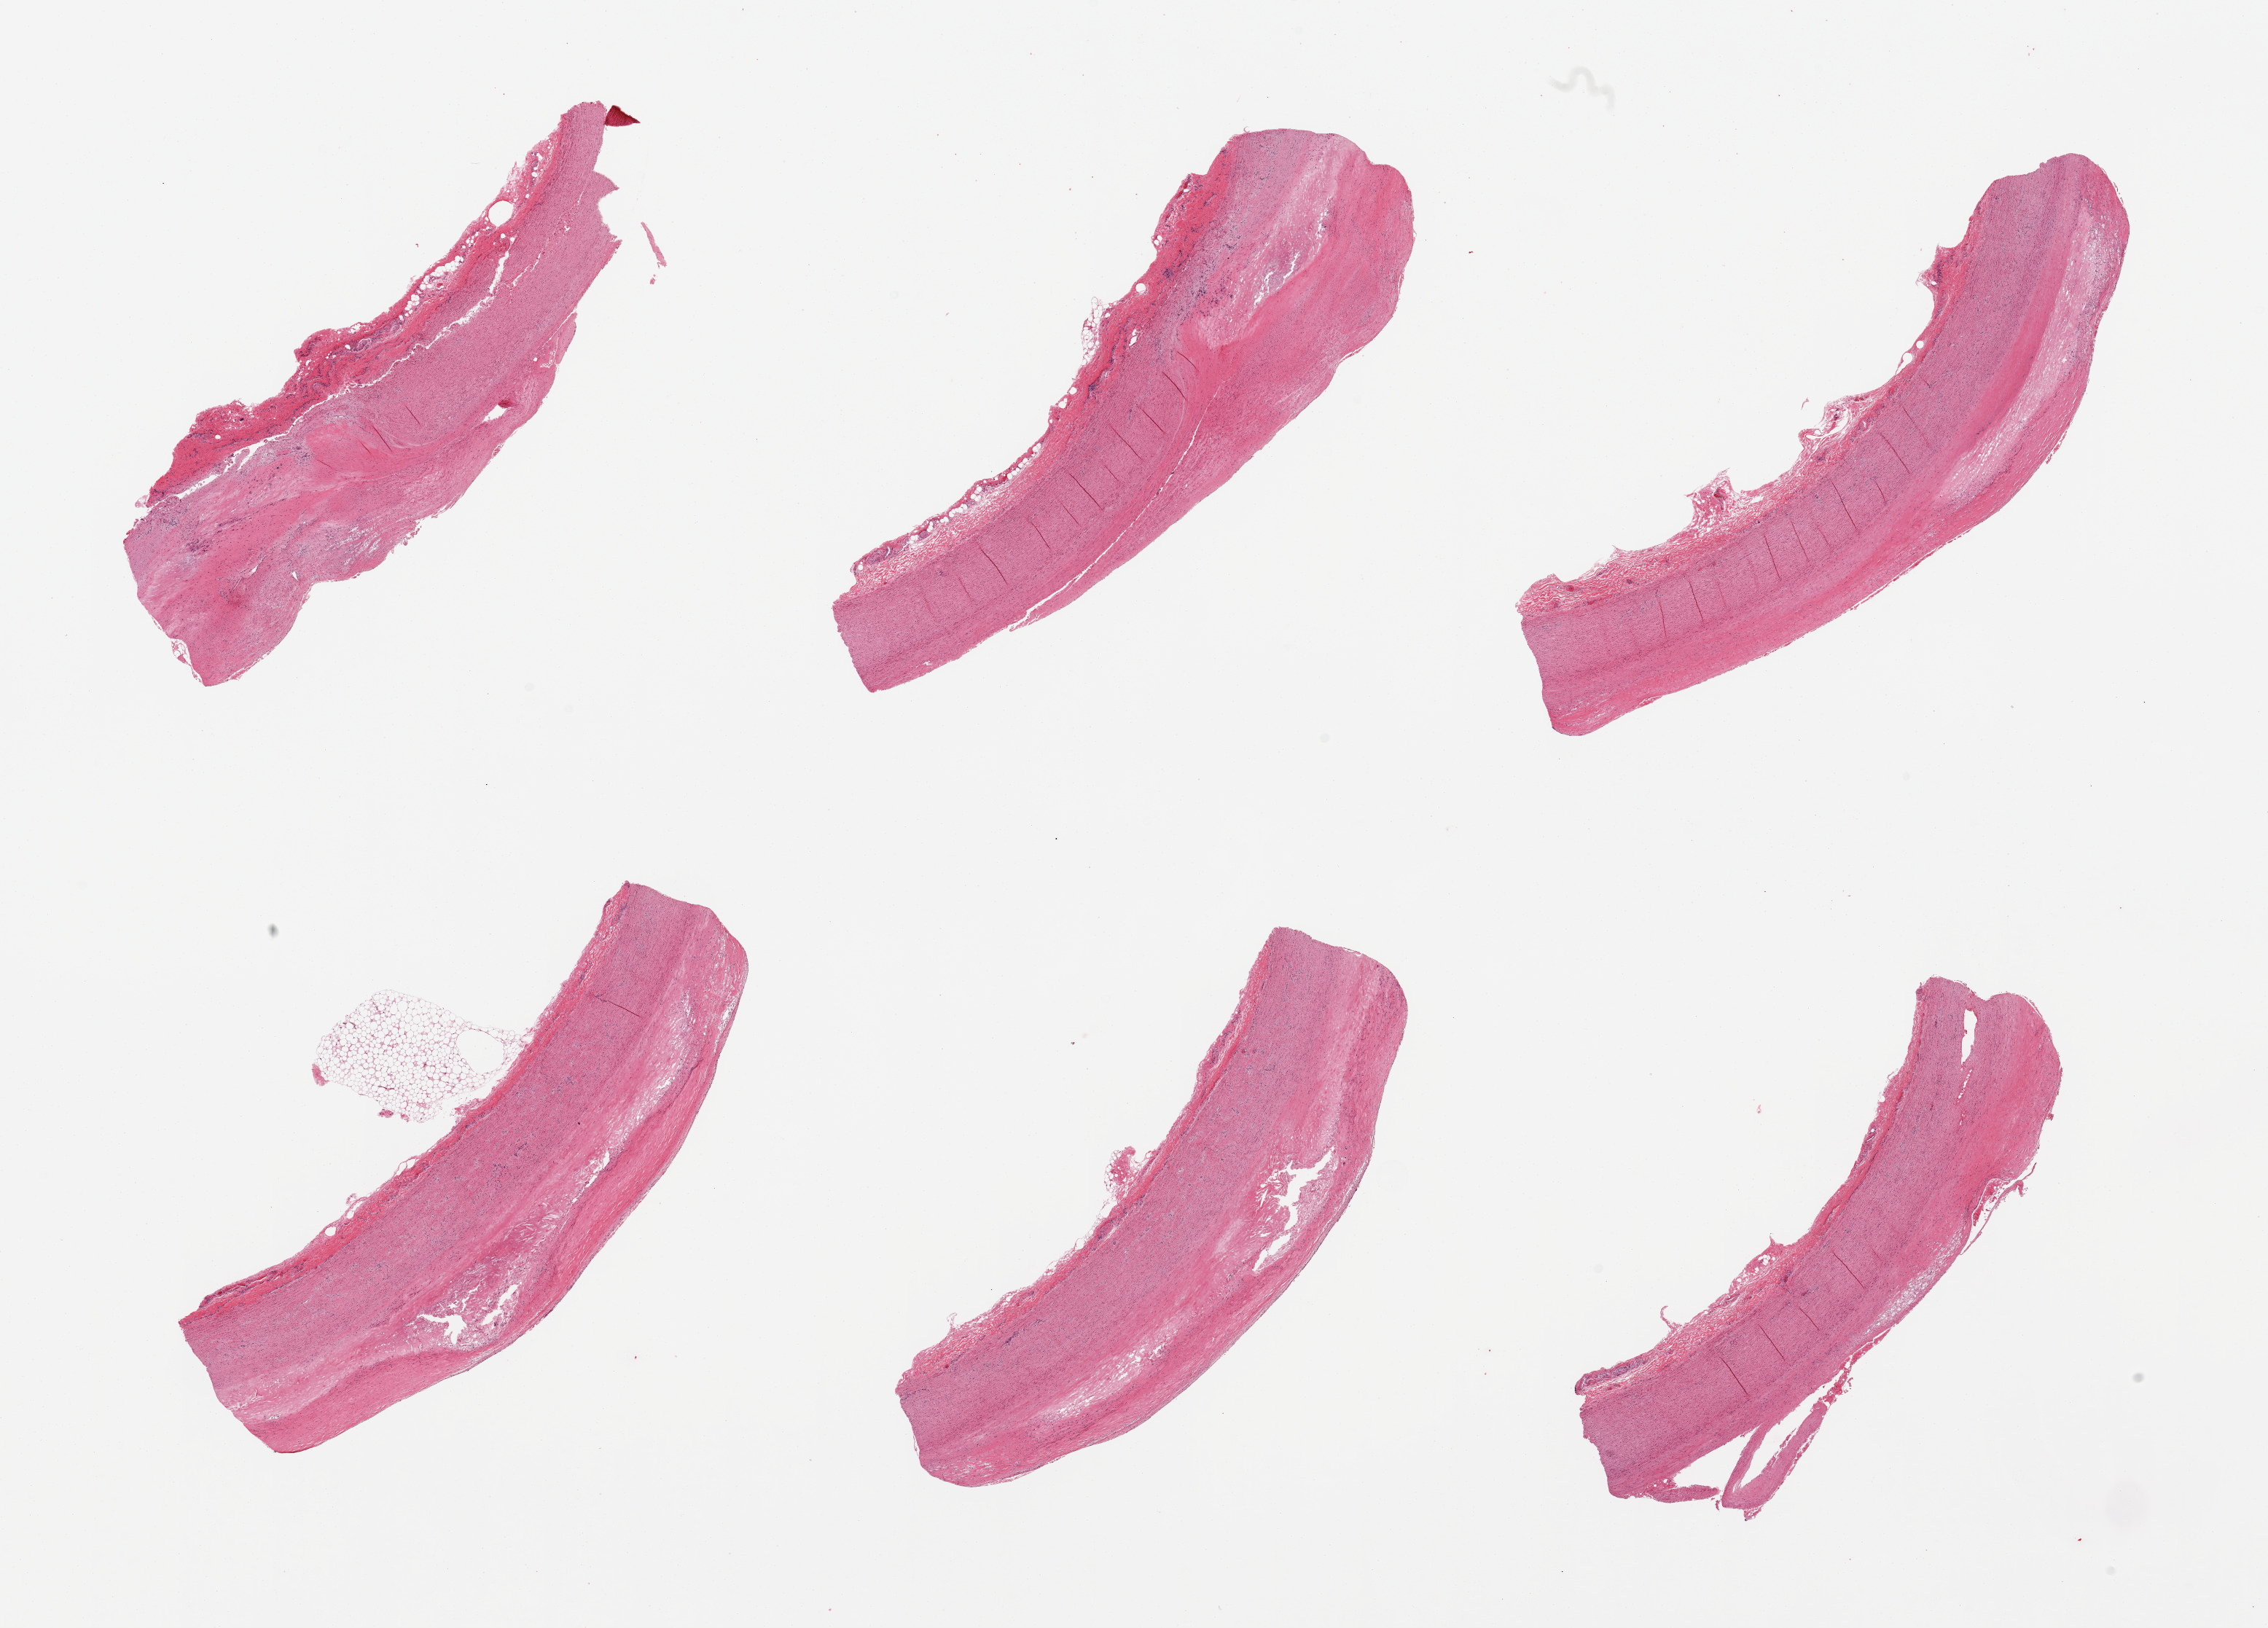
Digitized H&E-stained section, shown as a low-resolution overview of the whole scanned area (about 24.6 x 17.7 mm, from a 20x scan); PAXgene-fixed, paraffin-embedded tissue; sampled site (target tissue): aorta; donor tissue sample. Donor: male.
Reviewer comment on this tissue sample: 6 pieces, atherosis layer up to ~1mm.